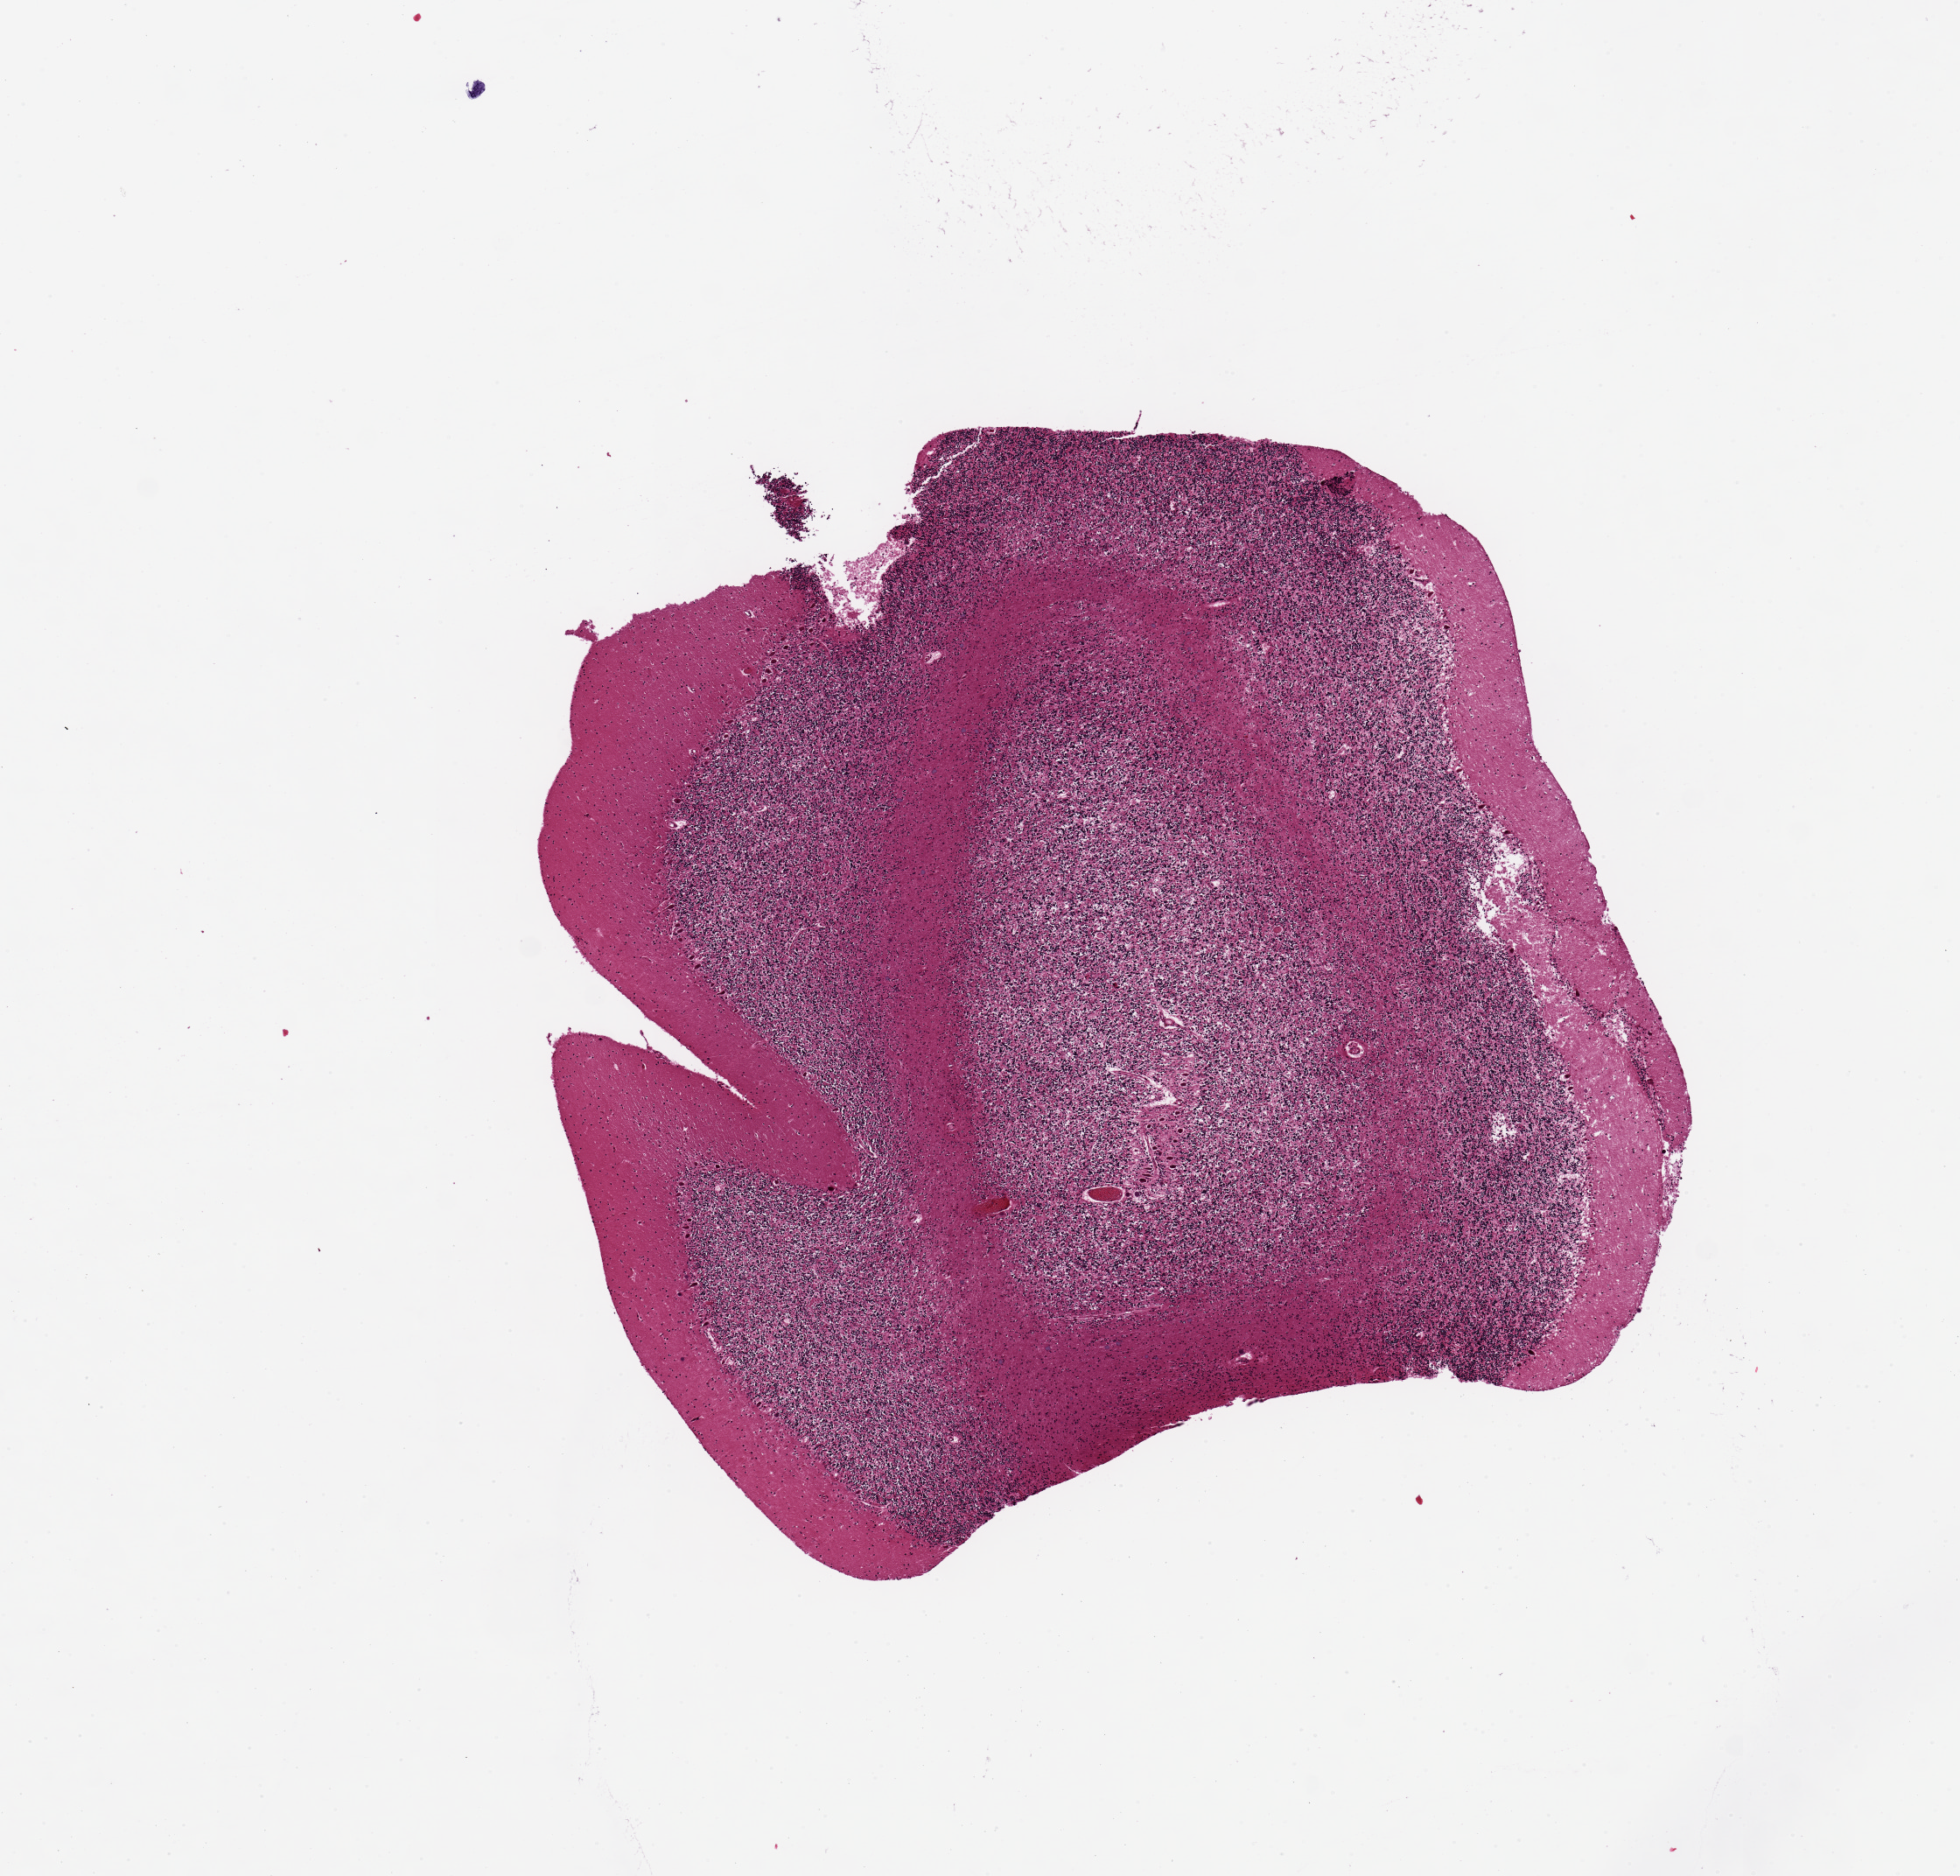
Whole-slide image, haematoxylin and eosin stain — low-resolution overview of the scanned area, about 8.9 x 8.5 mm. PAXgene-fixed, paraffin-embedded tissue. Target tissue: cerebellum. Donor tissue sample. Male donor.
- review note (as recorded): Most autolysis in inner layer. 4.6x4.8mm